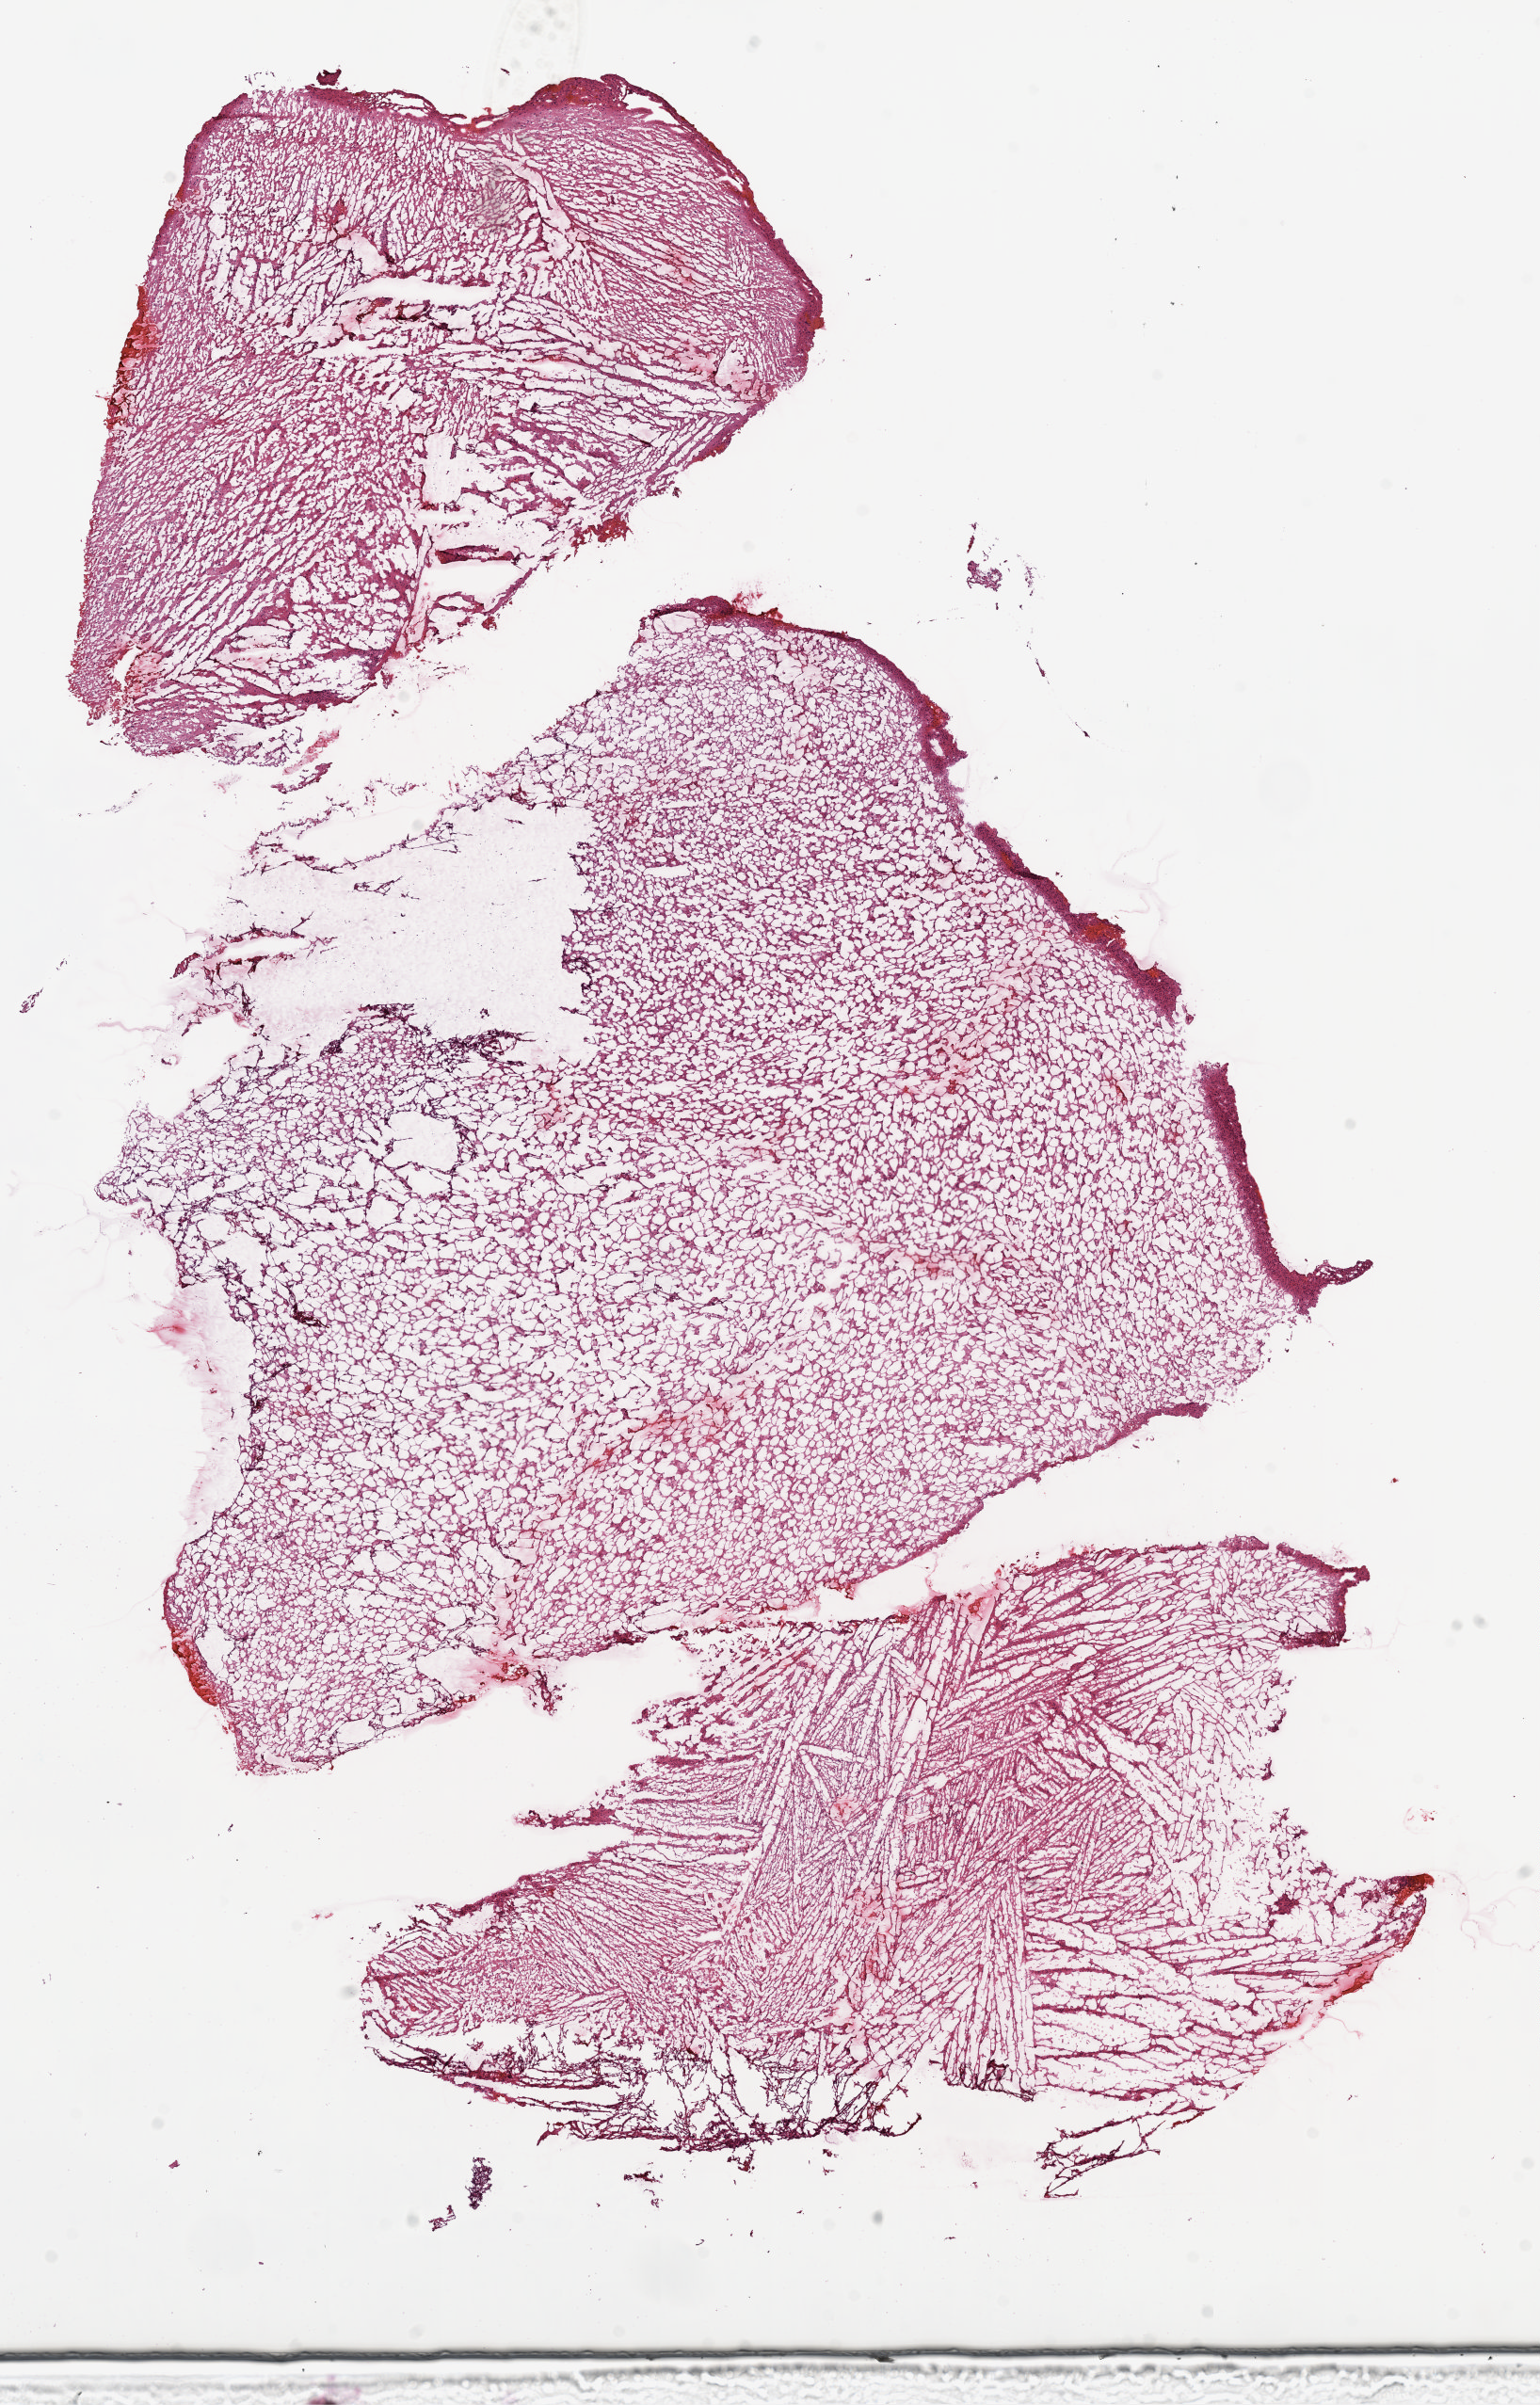
Digitized H&E-stained tissue section (whole slide), a low-resolution overview of the entire scanned area, about 13.1 x 20.5 mm. Frozen section from the top of the tissue portion. Sample: primary tumour, brain. Male patient; age at initial diagnosis 39 years. Histologic grade: G3 (poorly differentiated). Composition of this section per pathologist review: tumour cells 100%, tumour nuclei 75%, normal cells 0%, stromal cells 0%, necrosis 0%.
* pathologic diagnosis: Astrocytoma, anaplastic
* laterality: left